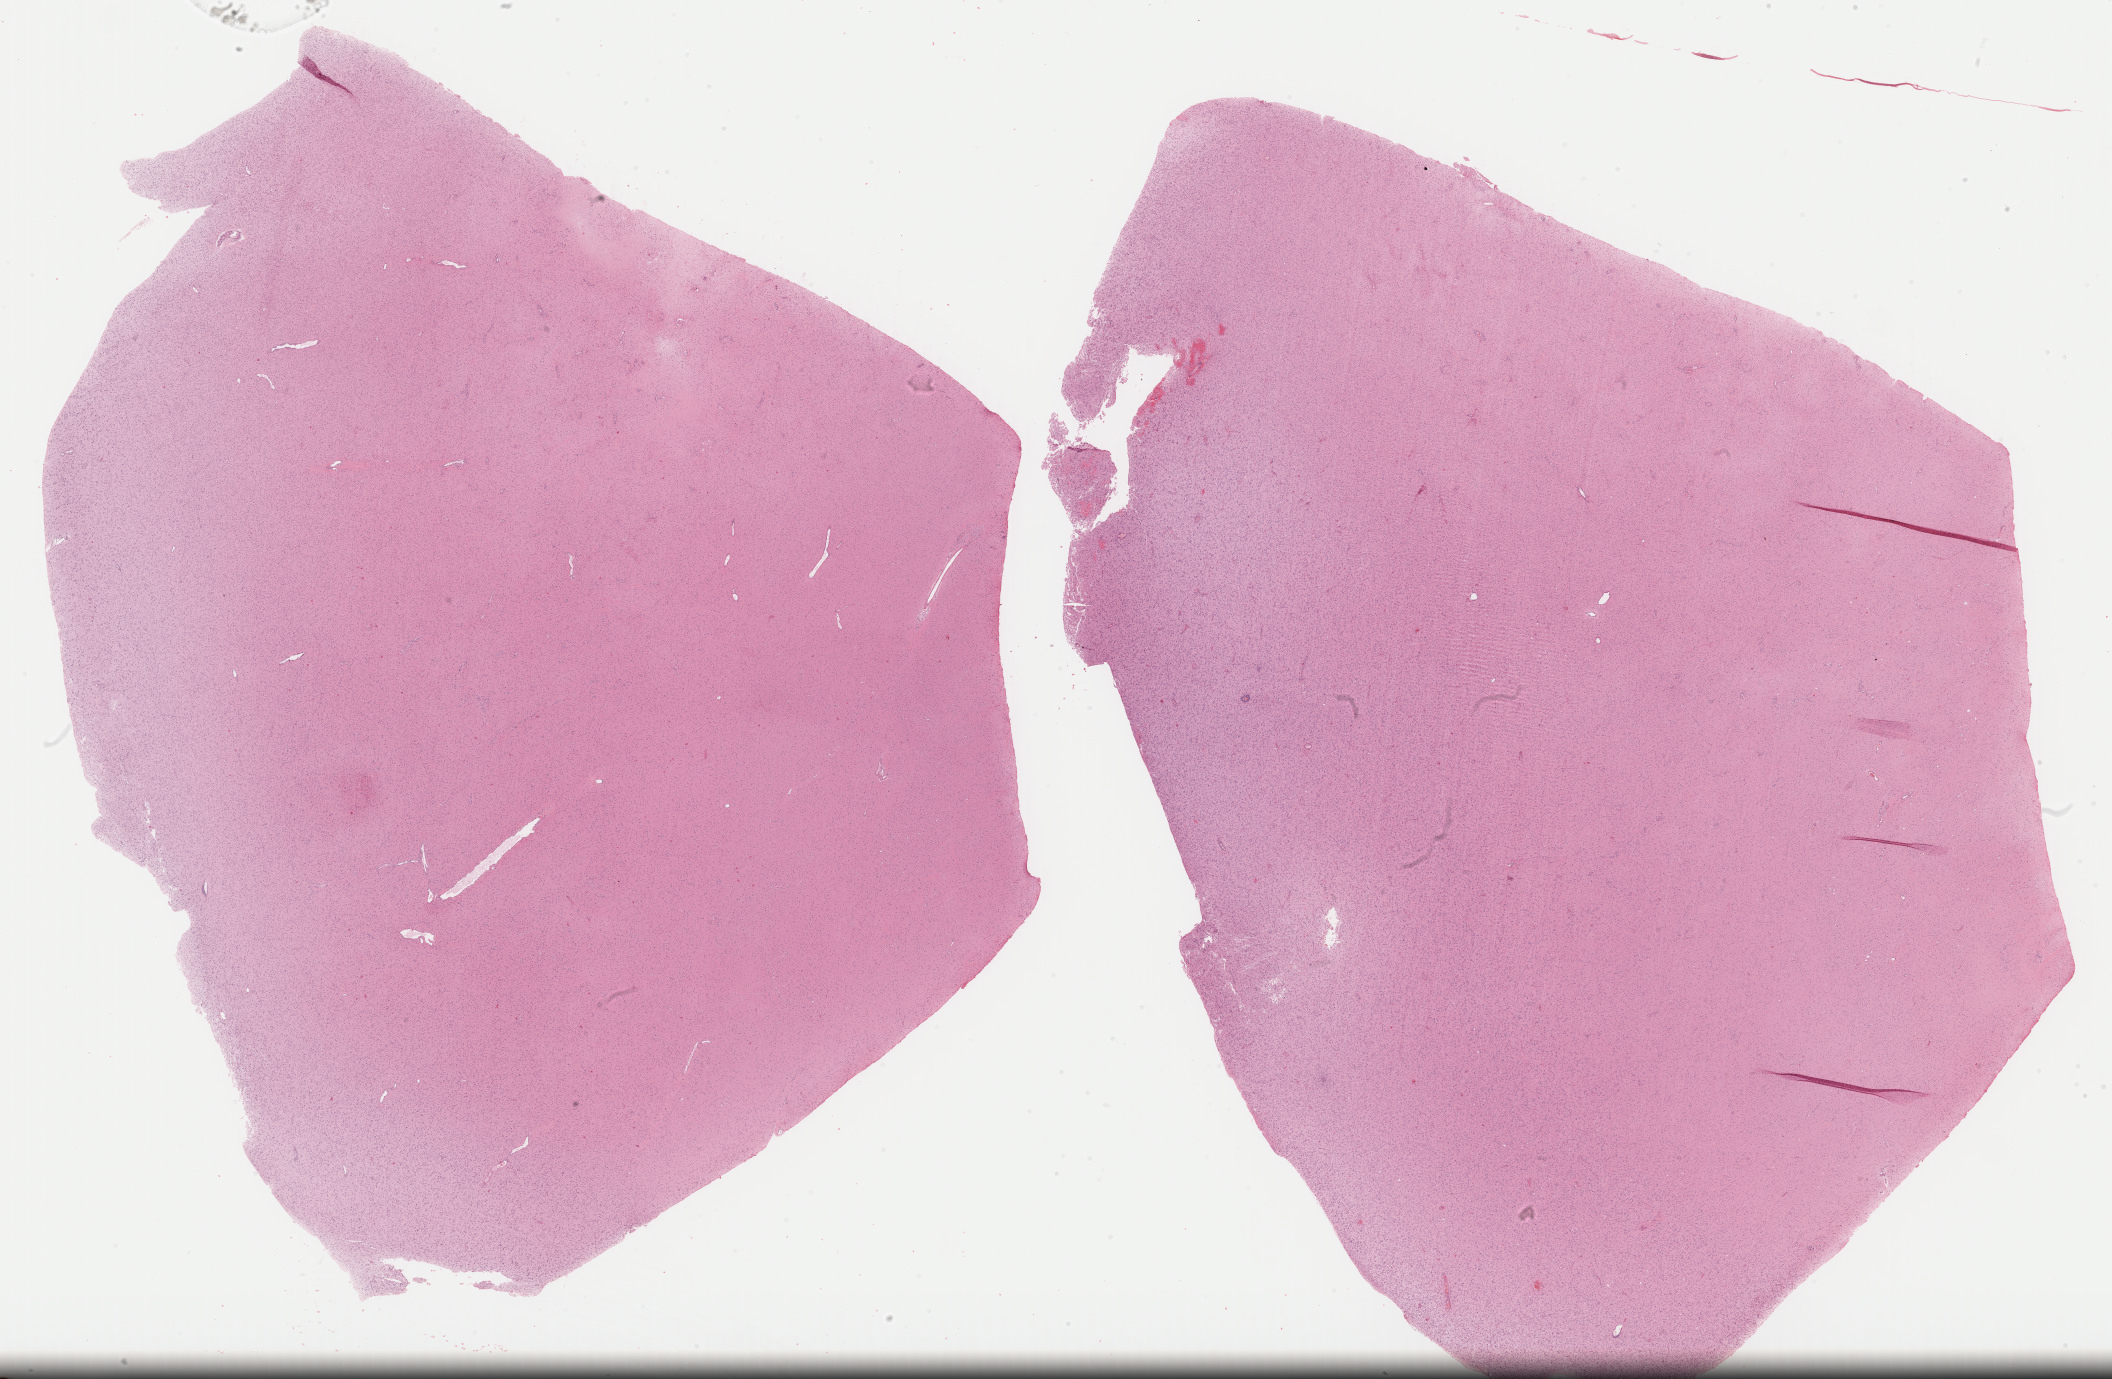
Whole-slide histology image, H&E, shown as a low-resolution overview of the whole scanned area (about 33.3 x 21.7 mm, acquisition: 40x scan). Formalin-fixed paraffin-embedded (FFPE) diagnostic section. Brain, primary tumour sample. Male, age 33 years at initial diagnosis. Histologic grade: G3 (poorly differentiated).
Histologic diagnosis: Astrocytoma, anaplastic. Laterality: right.